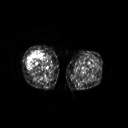
FDG PET of an extremity soft-tissue mass (from a PET/CT study), one axial slice; slice 218 of 311 in the series (ordered by position); 3.27 mm slice thickness; 128 × 128 image matrix, field of view 500 × 500 mm. Female patient, age 57 years. Case-level facts recorded for this patient, not image findings: histological type: pleiomorphic undifferentiated sarcoma; grade: high; site of the primary tumour: right quadricep.
Annotated regions visible in this slice (expert contour drawn on MRI and transferred to this co-registered scan by the dataset authors):
- tumour plus oedema (research contour): bounding box [x1, y1, x2, y2] px = [26, 51, 41, 68]